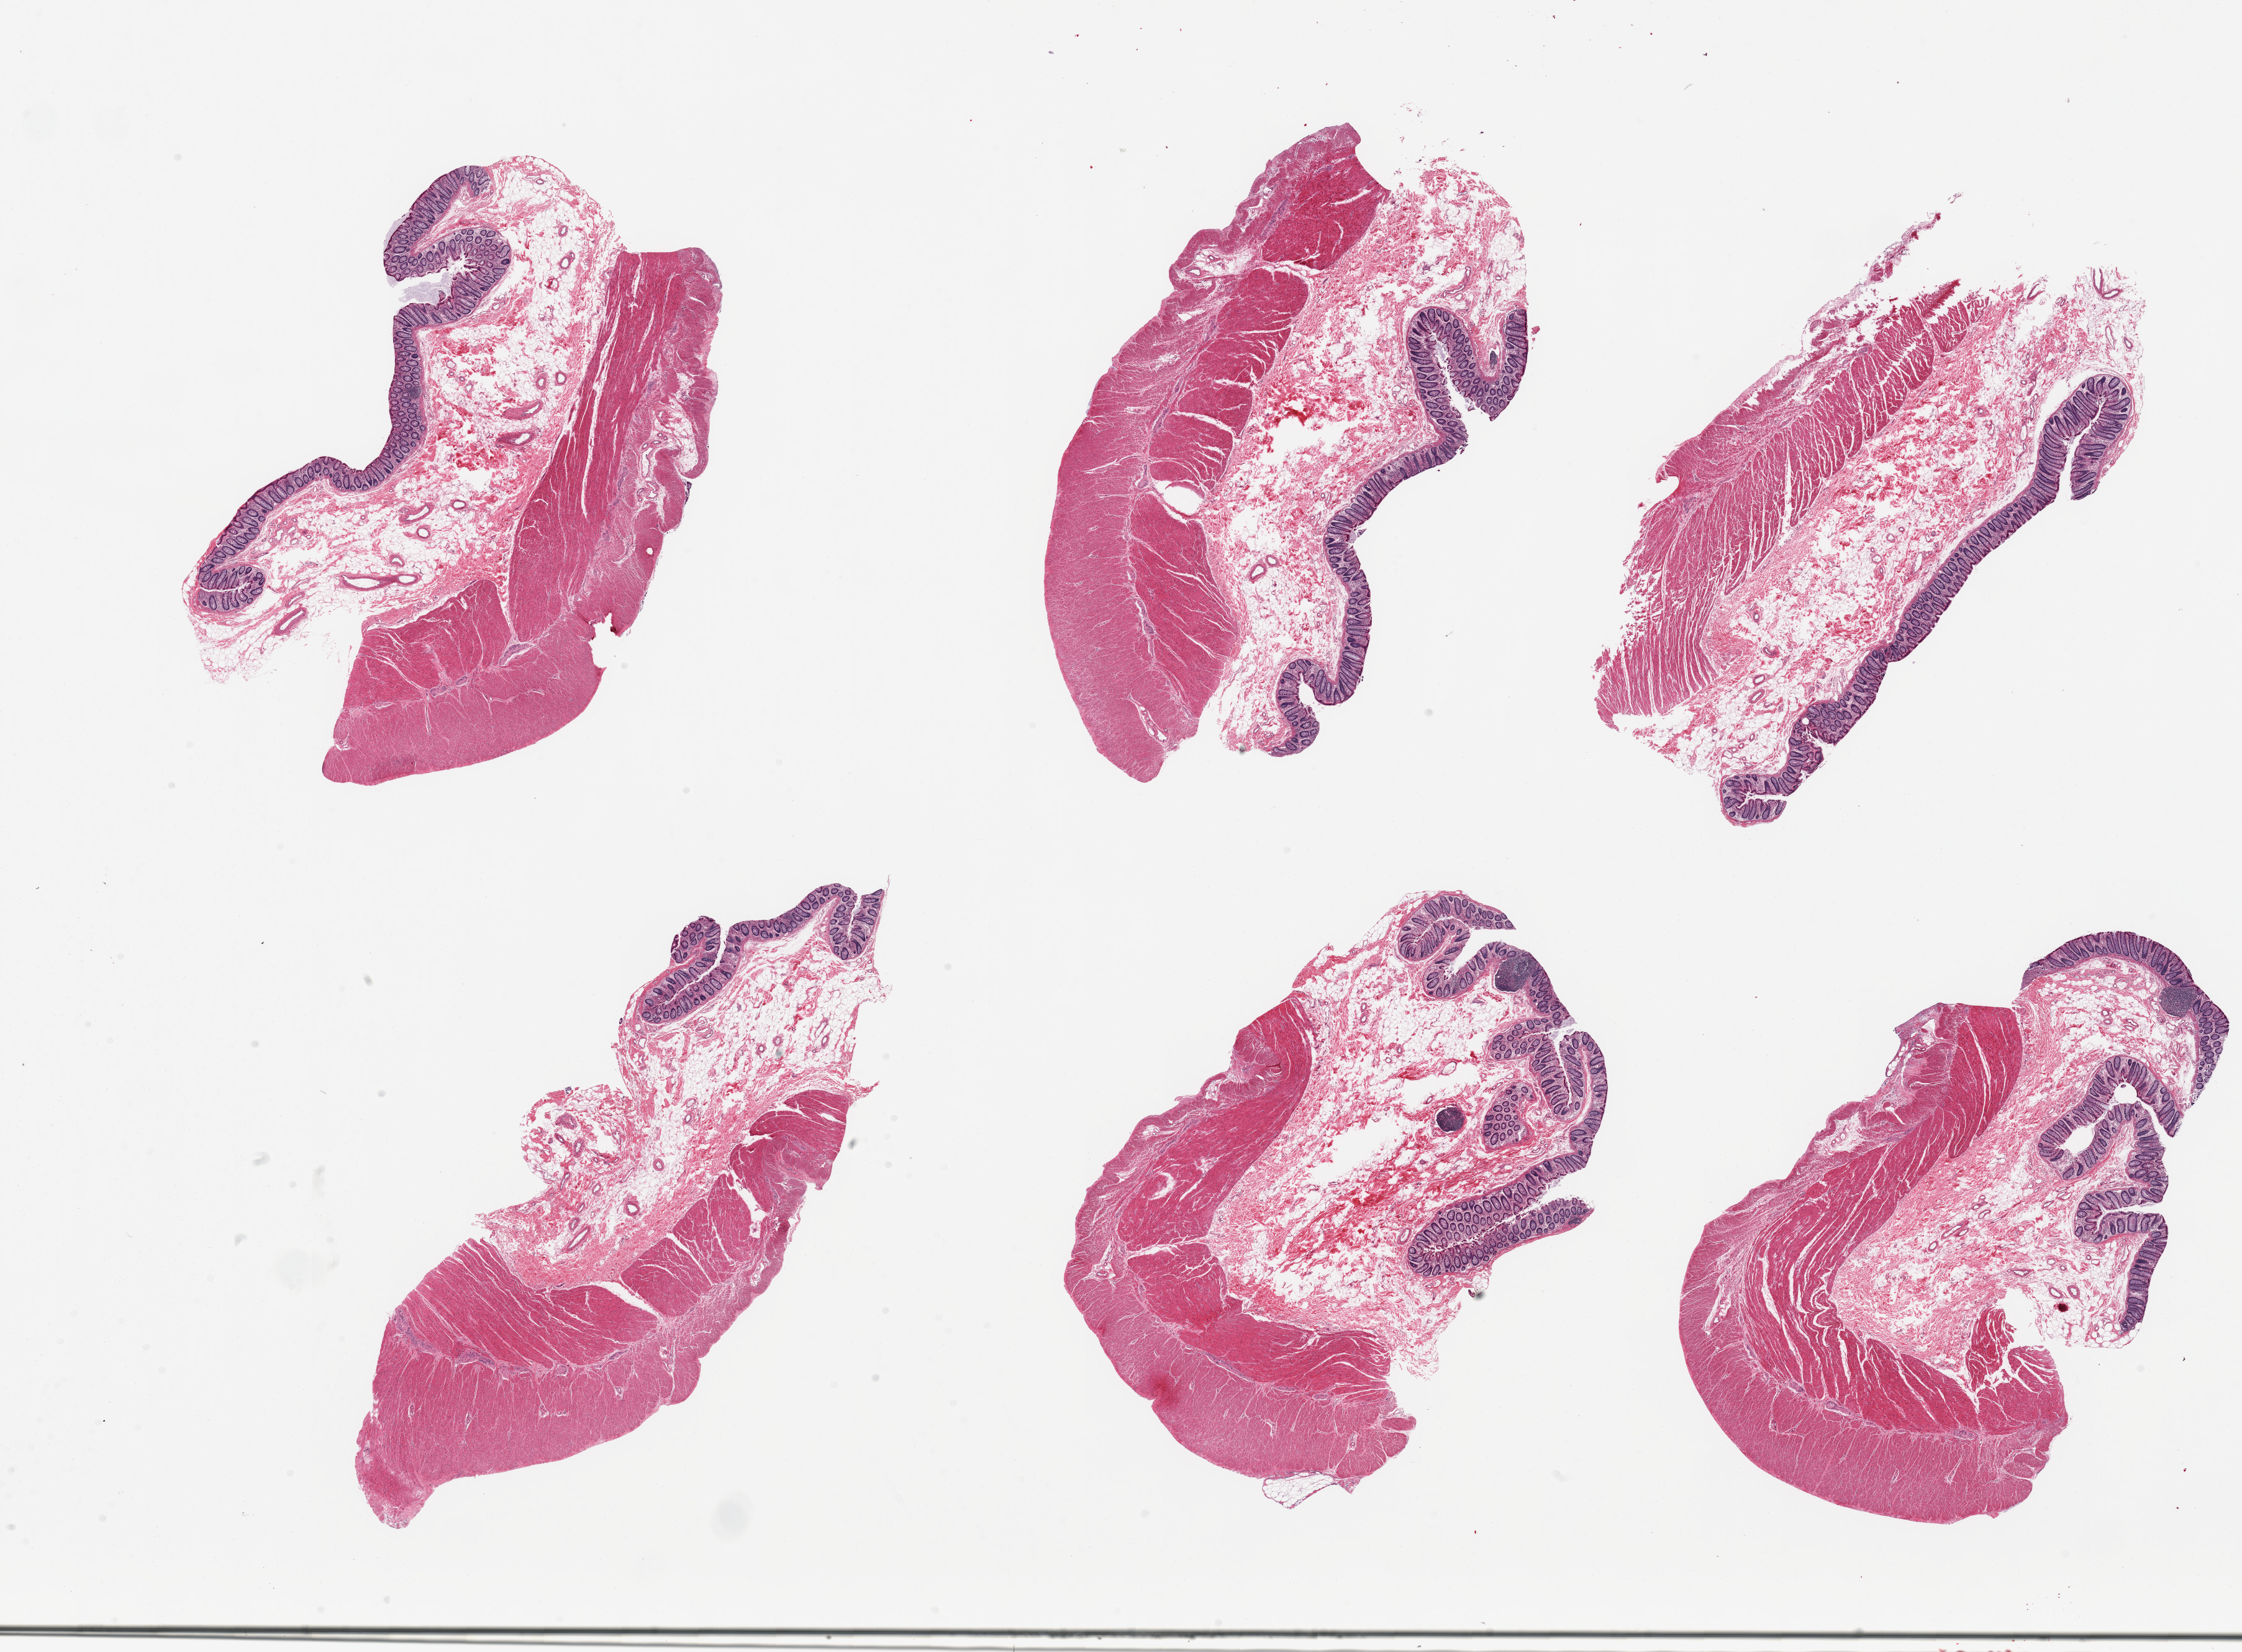
Whole-slide image, hematoxylin and eosin (H&E) stain, a low-resolution overview of the entire scanned area, about 28.5 x 21.0 mm (slide scanned at 20x). PAXgene-fixed, paraffin-embedded tissue. Sampled site (target tissue): transverse colon. Donor tissue sample. Male donor.
Reviewer comment on this tissue sample: 6 pieces; full thickness sections, focal serositis.